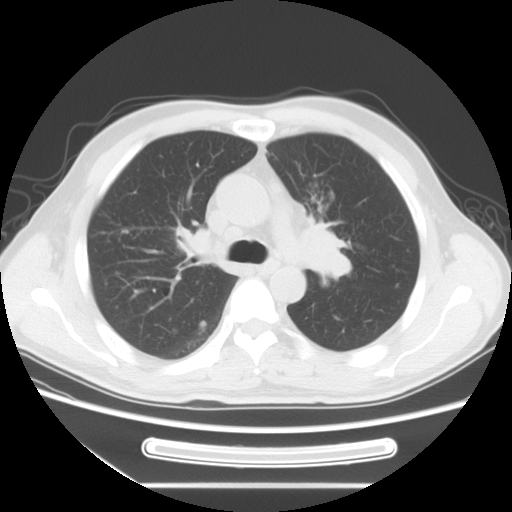
Chest CT, one axial slice; slice 48 of 71 in the series (ordered by position); lung window (W 1500 / L -600 HU); 5 mm slice thickness; 512 × 512 image matrix, field of view 366 × 366 mm. Male patient, age 51 years. Case-level facts recorded for this patient, not image findings: clinical TNM (as recorded): T1c N3 M0.
Annotated regions visible in this slice (rectangle marked by the reading radiologist):
- lung tumour (recorded histology: adenocarcinoma): bounding box <293,205,359,300> (left, top, right, bottom; pixels)